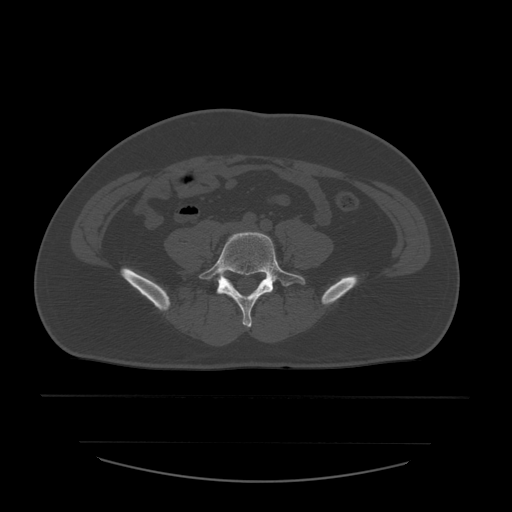
CT including the spine, one axial slice. Slice 122 of 532 in the series (ordered by position). Reconstruction kernel STANDARD. 120 kVp. Bone window (W 1800 / L 400 HU). 1.25 mm slice thickness. 512 × 512 image matrix, field of view 441 × 441 mm. Patient age 44 years. From the clinical record (not read from this slice): primary cancer: soft tissue sarcoma.
Structures marked on this image (semi-automatically segmented with operator editing):
- L5 vertebra: bounding box <199,232,306,328> (left, top, right, bottom; pixels)